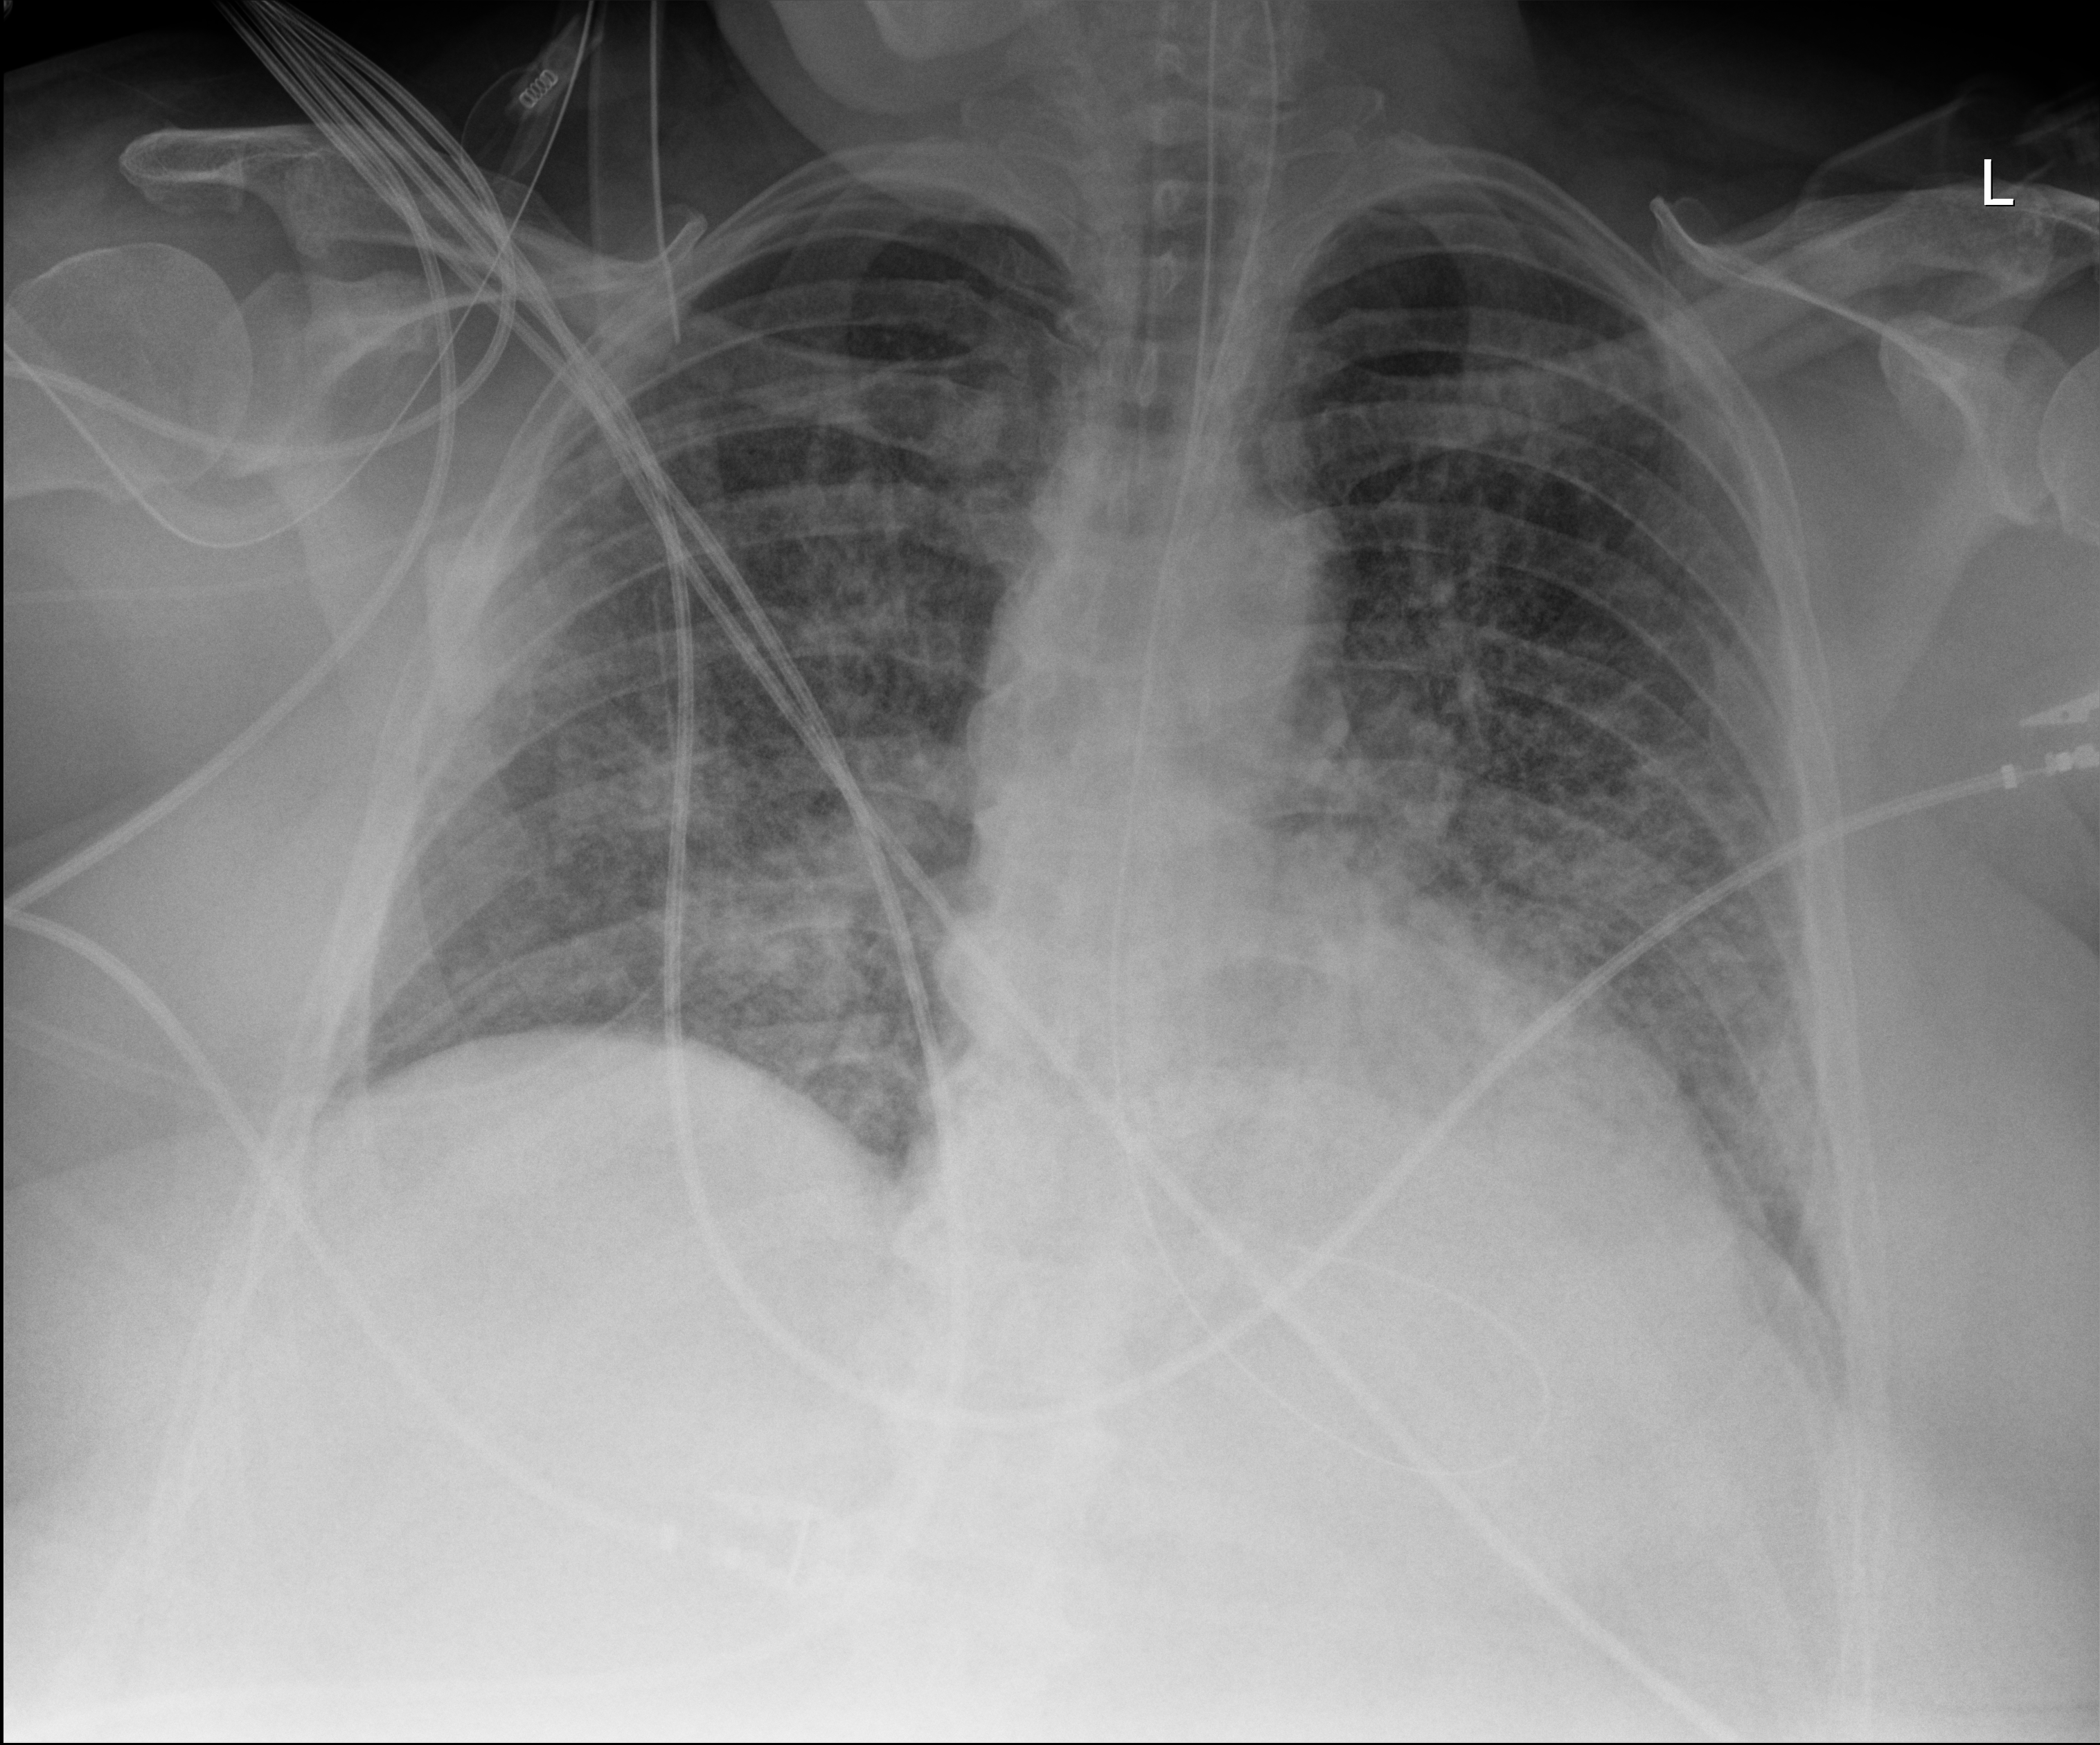
Chest X-ray, anteroposterior (AP) projection. Adult patient hospitalised with COVID-19, age 18–59 years.
Admission-level facts for this patient (not findings on this image; timing relative to this image not recorded): admitted to intensive care during this hospital stay: yes.